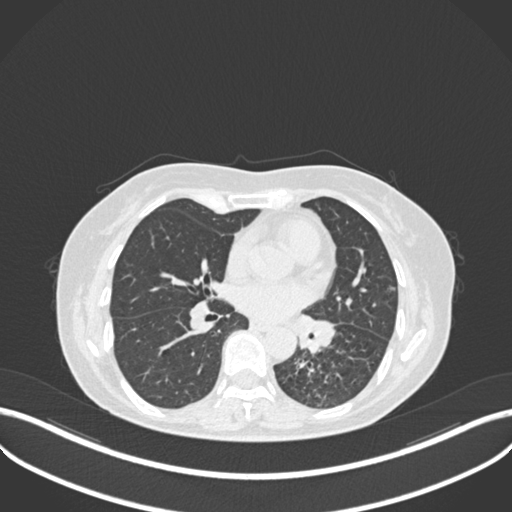
Chest CT, one axial slice; slice 124 of 270 in the series (ordered by position); lung window (W 1500 / L -600 HU); 512 × 512 image matrix. Female patient, age 63 years. Case-level facts recorded for this patient, not image findings: clinical TNM (as recorded): T1b N0 M0.
Structures marked on this image (bounding box drawn by a radiologist):
- lung tumour (recorded histology: adenocarcinoma): bounding box [x1, y1, x2, y2] px = [285, 309, 346, 360]